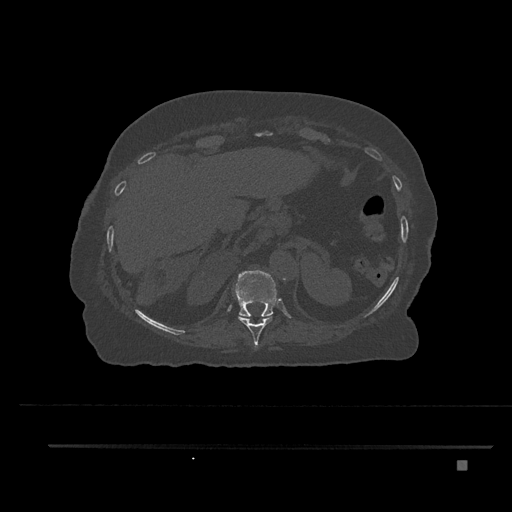
CT including the spine, one axial slice. Position 333 of 797 along the scan axis. 120 kVp. Bone window (W 1800 / L 400 HU). 0.5 mm slice thickness. 512 × 512 image matrix, field of view 437 × 437 mm. Female patient, age 76 years. Case-level facts recorded for this patient, not image findings: primary cancer: lung; vertebrae with lytic lesions (as recorded): T11, L3.
Annotated regions visible in this slice (semi-automatically segmented with operator editing):
- T10 vertebra: bounding box (x1, y1, x2, y2) in pixels: (238, 315, 272, 347)
- T11 vertebra: (234, 270, 277, 317)